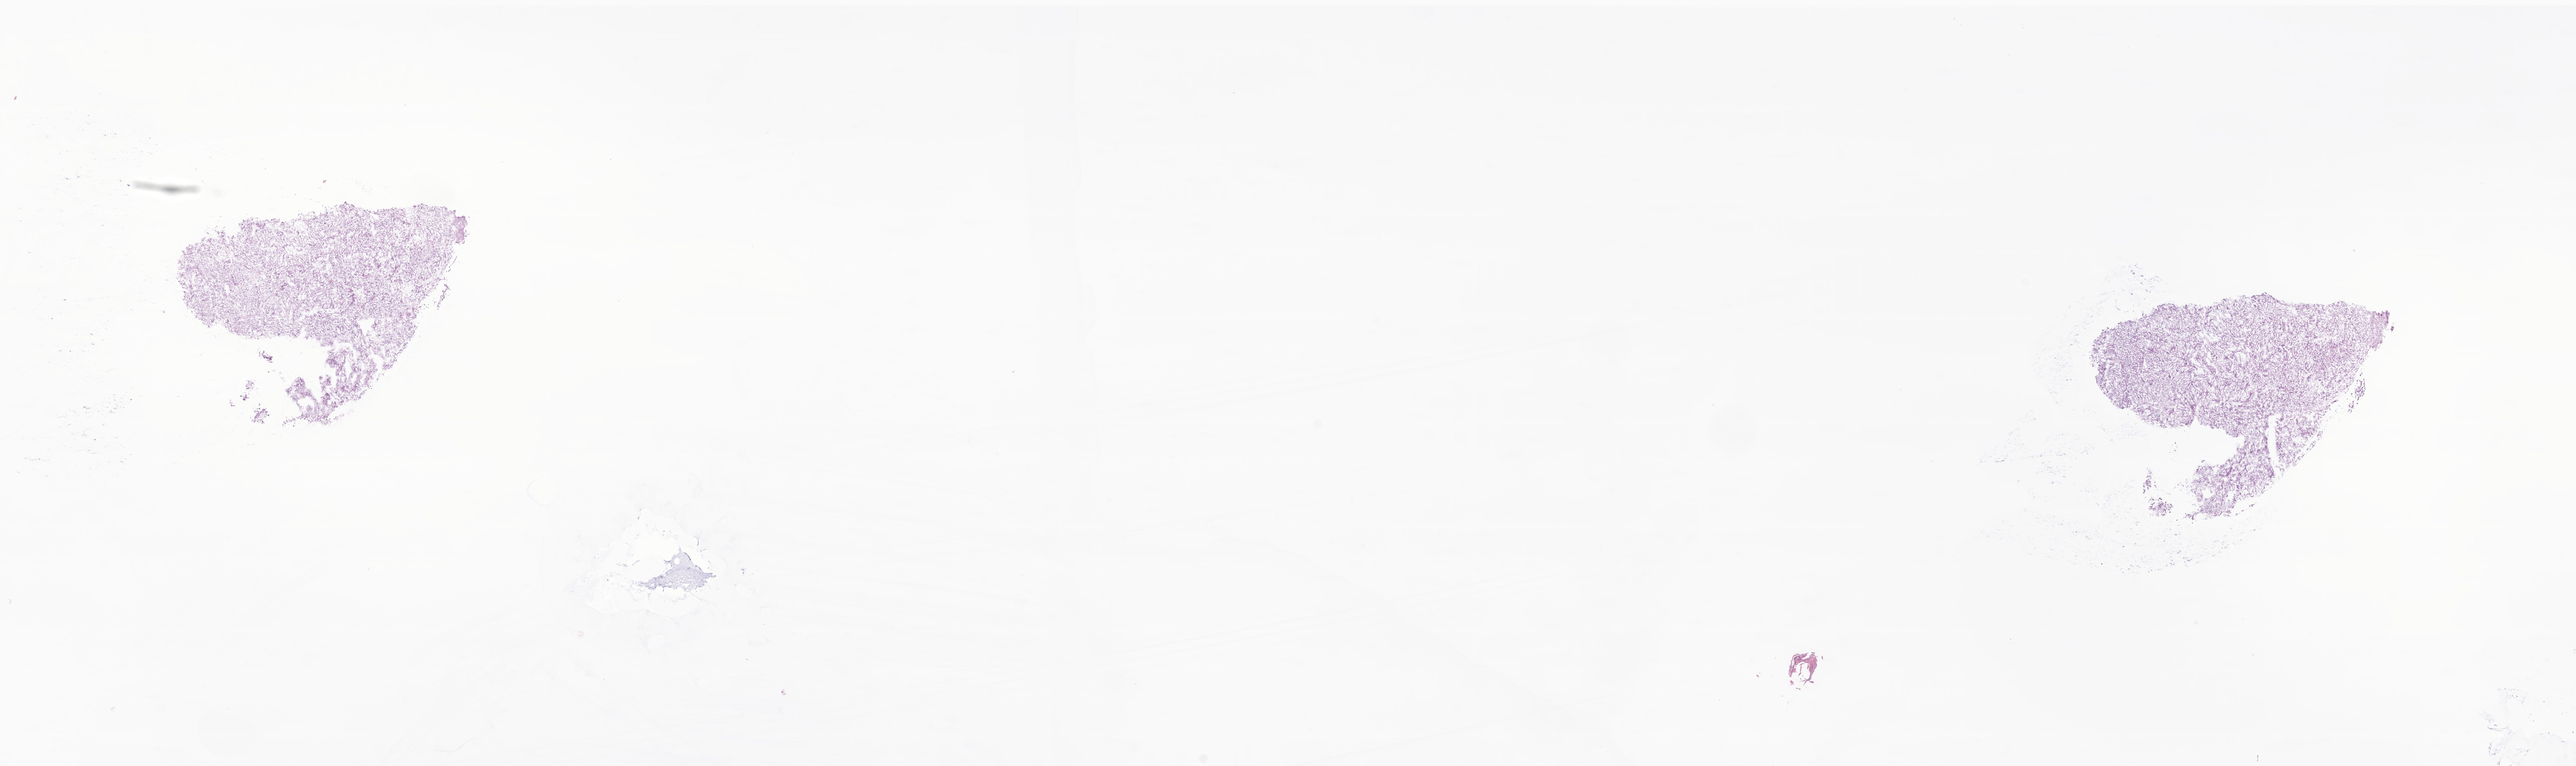
Haematoxylin and eosin whole-slide image of tumor tissue from the brain — low-resolution overview of the scanned area, about 26.4 x 7.8 mm. Cryosection (OCT / tissue freezing medium). Female patient, age 216 months (18 years).
Diagnosis: Glioma, malignant.